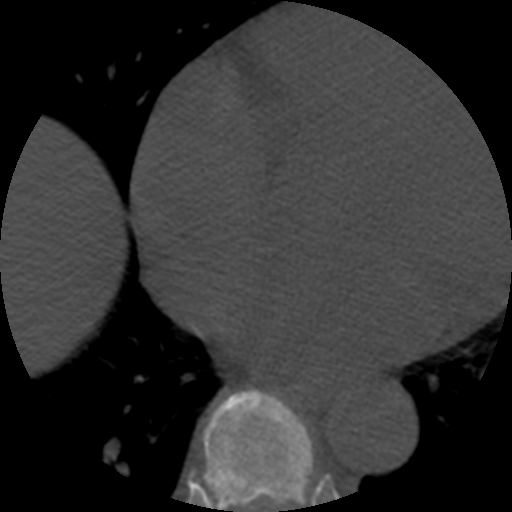
CT including the spine, one axial slice. Slice 323 of 508 in the series (ordered by position). 120 kVp. Bone window (W 1800 / L 400 HU). 512 × 512 image matrix, field of view 160 × 160 mm. Patient age 57 years. Case-level facts recorded for this patient, not image findings: primary cancer: prostate.
Outlined on this slice (semi-automatic segmentation, software-assisted and operator-edited):
- T7 vertebra: bounding box <193,390,313,512> (left, top, right, bottom; pixels)